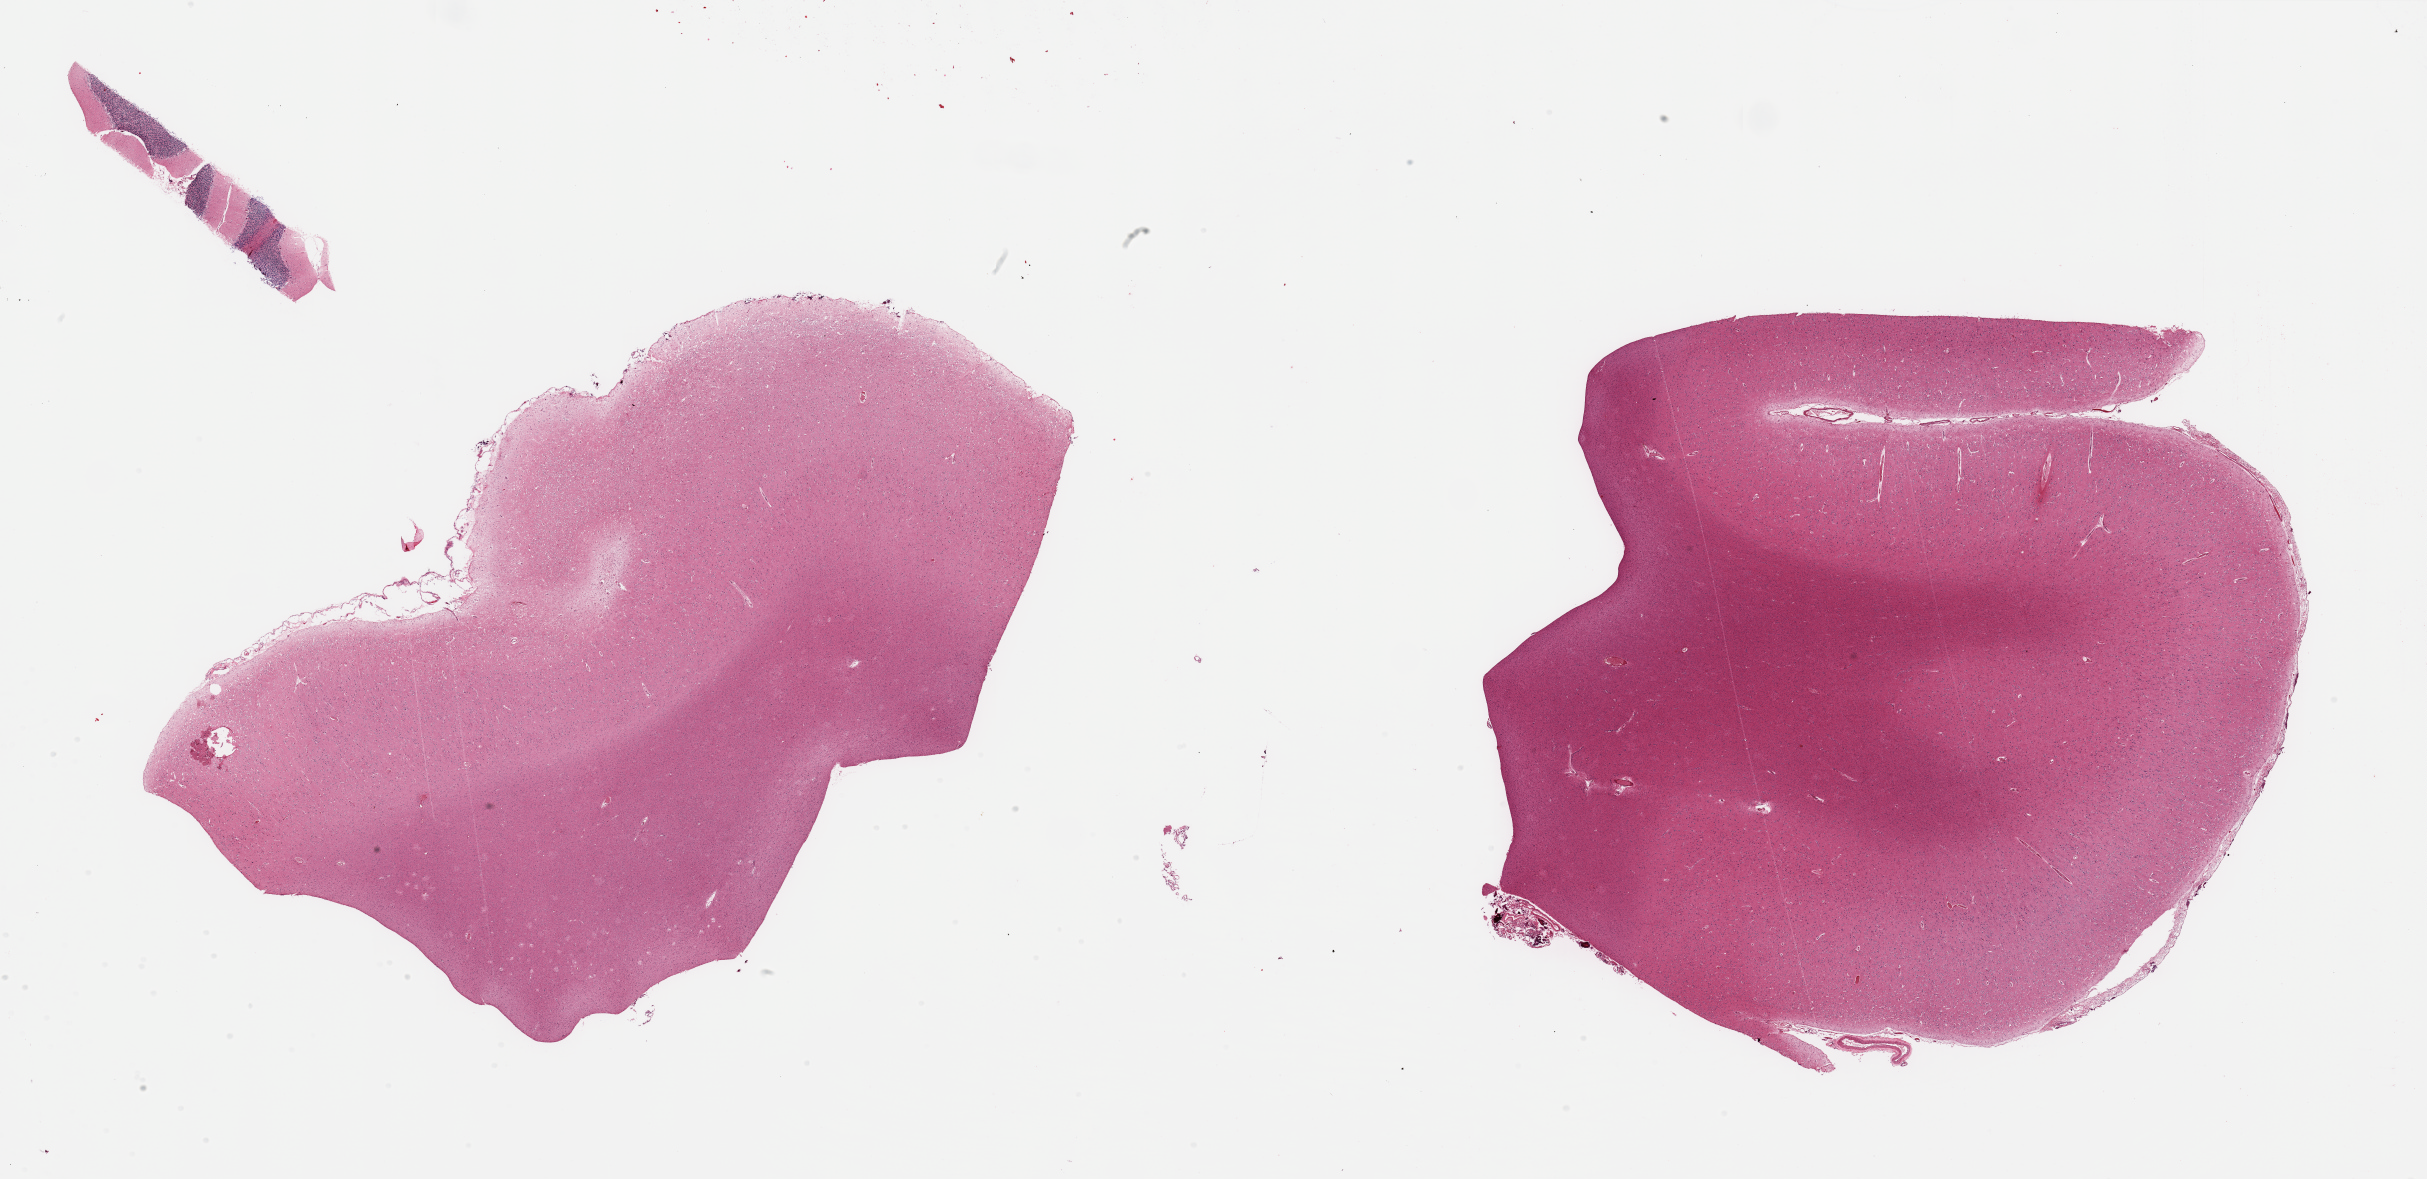
Whole-slide image, hematoxylin and eosin (H&E) stain, brightfield, whole scanned area (about 38.4 x 18.7 mm, acquisition: 20x scan) shown as a low-resolution overview. PAXgene-fixed, paraffin-embedded tissue. Sampled site (target tissue): cerebral cortex. Donor tissue sample. Donor sex: male.
Pathologist's review note for this sample: 2 pieces; attached meninges, focal calcifications, detached fragment of cerebellum (floater).